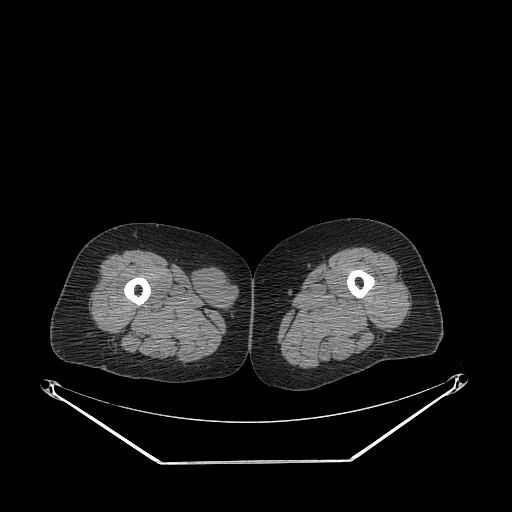
CT of an extremity soft-tissue mass (from a PET/CT study), one axial slice; slice 238 of 311 in the series (ordered by position); reconstruction kernel STANDARD; 140 kVp; soft-tissue window (W 400 / L 40 HU); 3.75 mm slice thickness; 512 × 512 image matrix, field of view 500 × 500 mm. Female patient. From the clinical record (not read from this slice): histological type: leiomyosarcoma; grade: intermediate; site of the primary tumour: parascapusular.
Annotated regions visible in this slice (expert contour drawn on MRI and transferred to this co-registered scan by the dataset authors):
- gross tumour volume including surrounding oedema: bounding box (x1, y1, x2, y2) in pixels: (192, 267, 238, 314)
- gross tumour volume (mass): (192, 267, 238, 314)